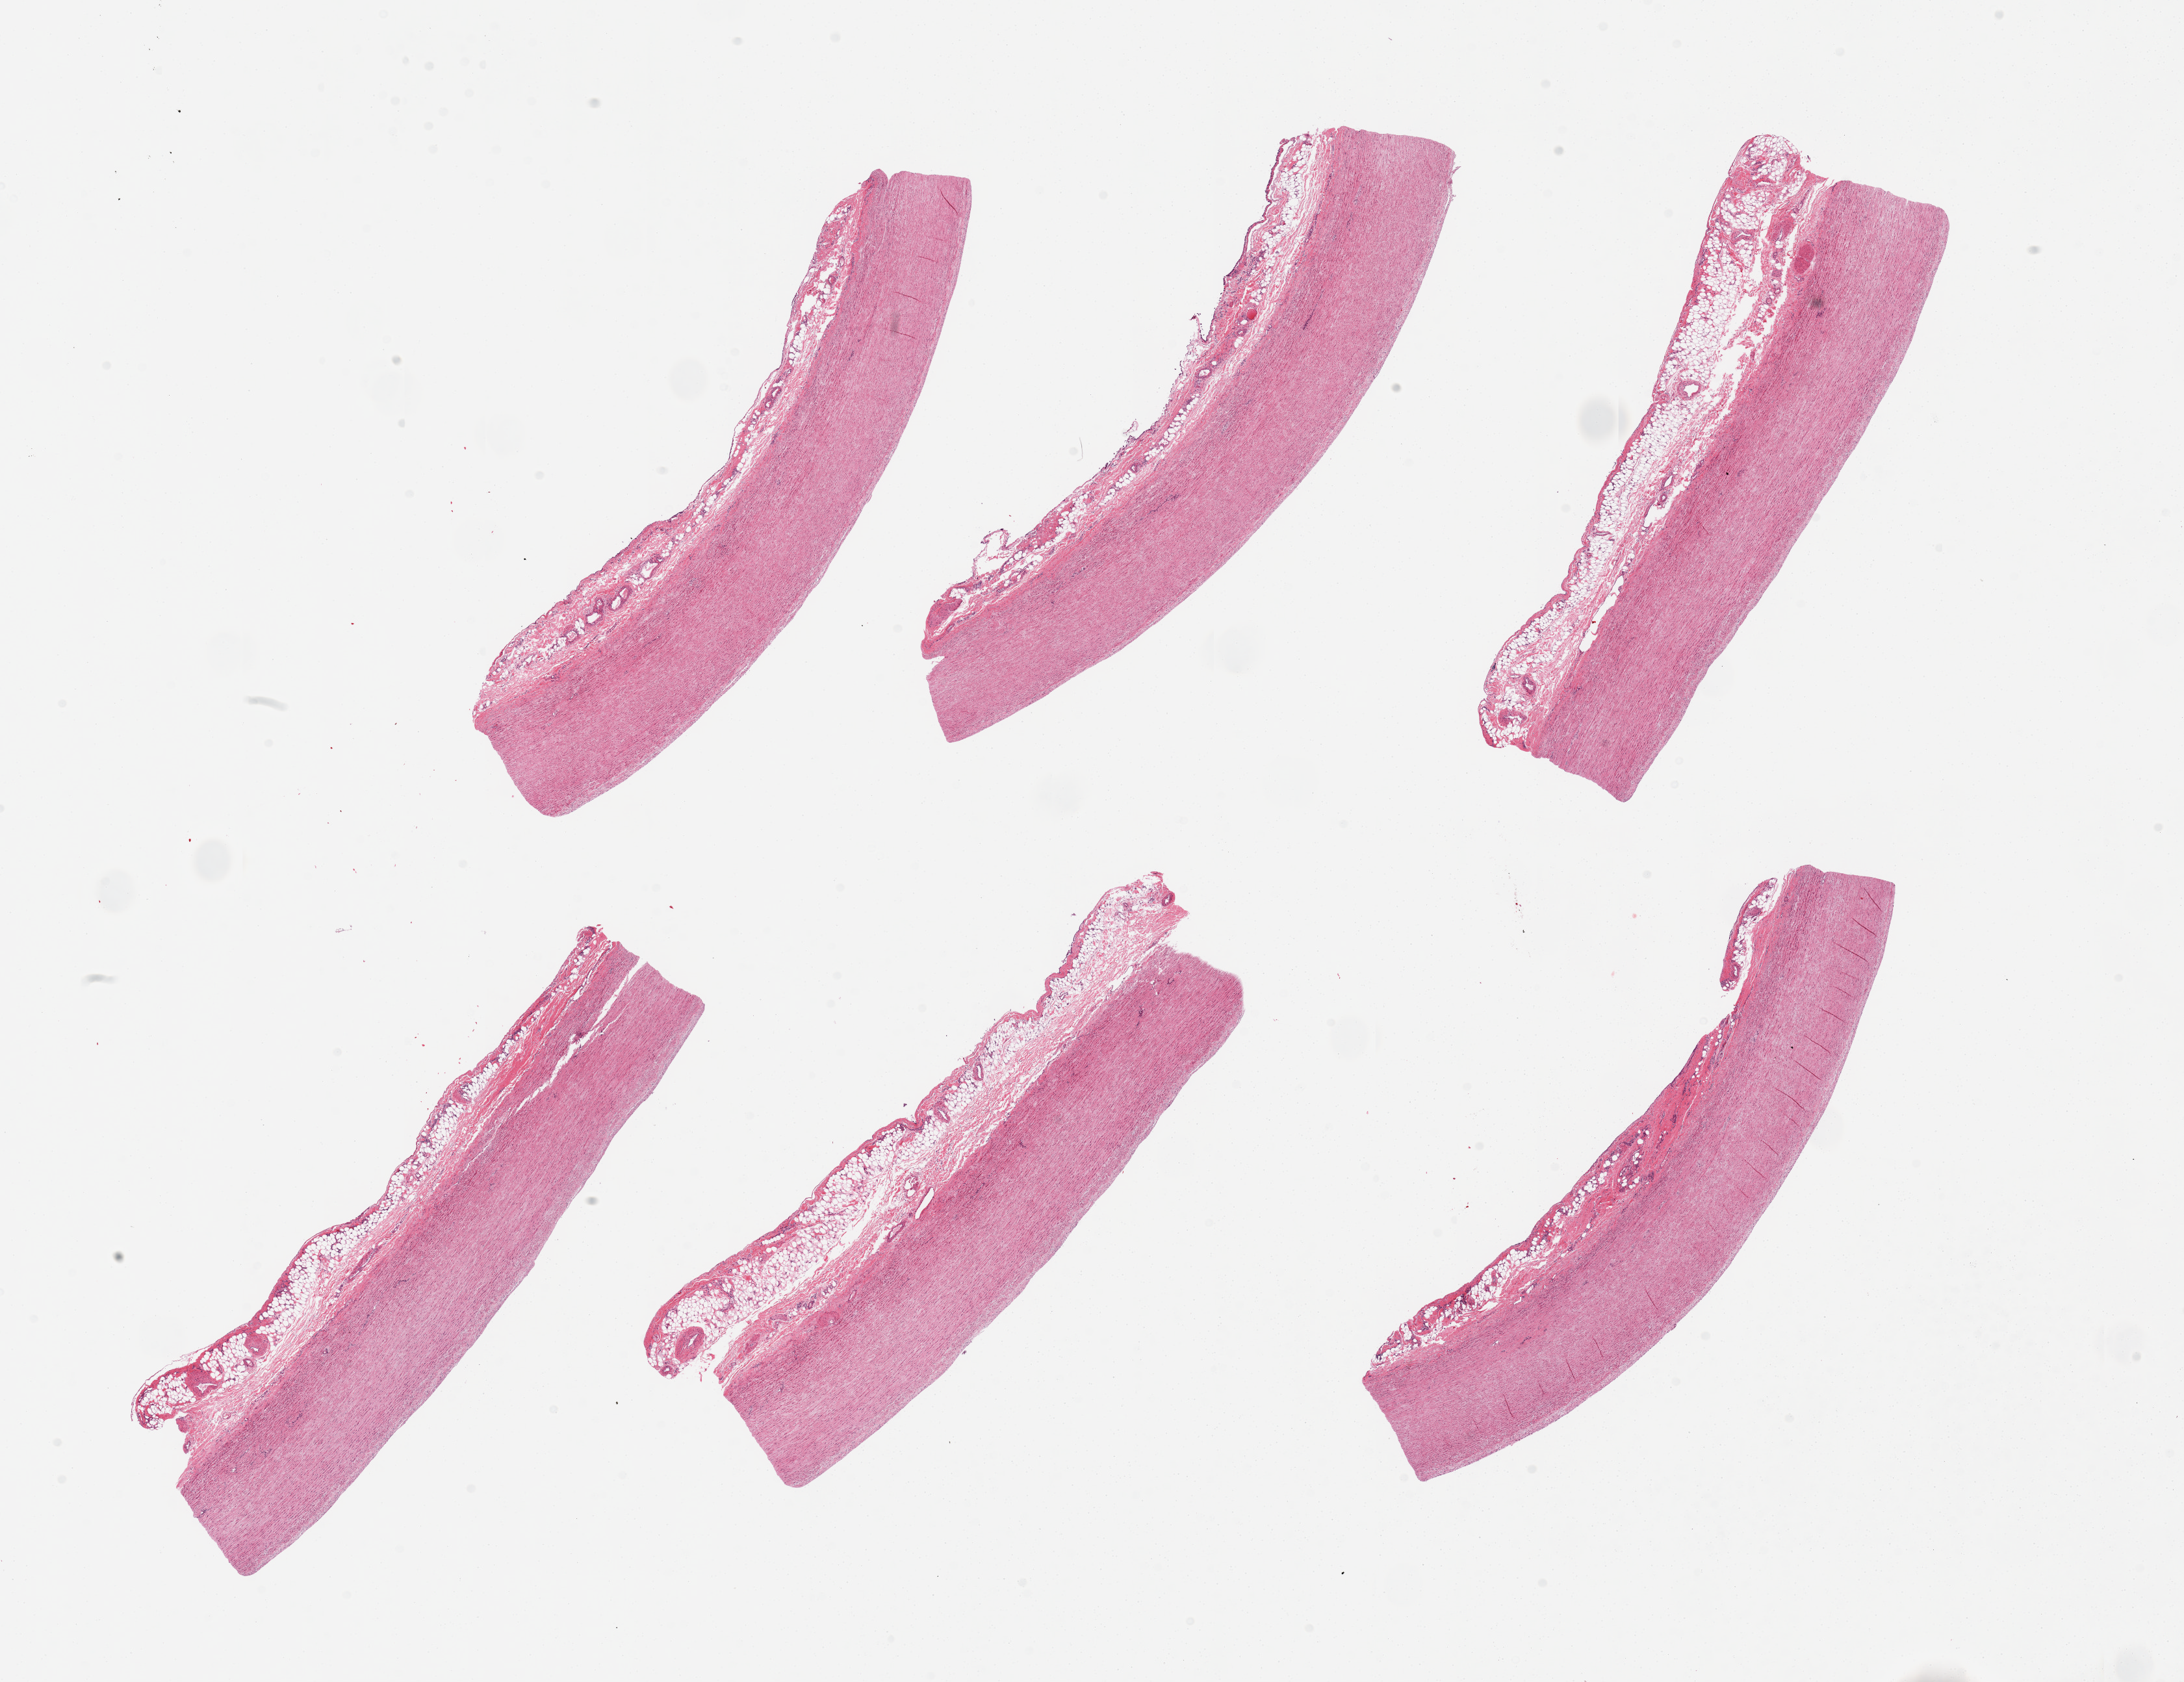
Hematoxylin and eosin (H&E) whole-slide image, shown as a low-resolution overview of the whole scanned area (about 26.6 x 20.5 mm); PAXgene-fixed paraffin-embedded (PFPE) section; target tissue: aorta; donor tissue sample. Donor: female.
• reviewer comment on this tissue sample: 6 pieces, includes 20-40% attached adventitia/fat